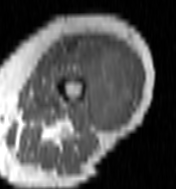
MRI of an extremity soft-tissue mass, one axial slice. MR volume resampled by the dataset authors to the PET/CT grid (not the native acquisition matrix). 176 × 189 image matrix, field of view 172 × 185 mm. Female patient. From the clinical record (not read from this slice): histological type: undifferentiated – high grade; grade: high; site of the primary tumour: left thigh.
Outlined on this slice (expert contour drawn on MRI and transferred to this co-registered scan by the dataset authors):
- gross tumour volume including surrounding oedema: box from (x=59, y=39) to (x=138, y=126) px
- gross tumour volume (mass): (x=73, y=39)–(x=136, y=126)